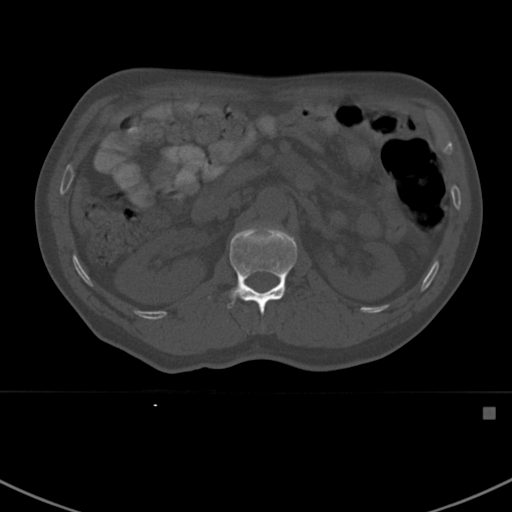
CT including the spine, one axial slice; slice 307 of 412 in the series (ordered by position); bone window (W 1800 / L 400 HU); 512 × 512 image matrix, field of view 358 × 358 mm. Male patient, age 59 years. From the clinical record (not read from this slice): primary cancer: prostate.
Structures marked on this image (semi-automatic segmentation, software-assisted and operator-edited):
- L1 vertebra: bounding box [x1, y1, x2, y2] px = [209, 224, 298, 331]